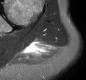
MRI of an extremity soft-tissue mass, one axial slice. Slice 19 of 30 in the series (ordered by position). STIR. MR volume resampled by the dataset authors to the PET/CT grid (not the native acquisition matrix). 3.27 mm slice thickness. 86 × 80 image matrix, field of view 84 × 78 mm. Female patient. Case-level facts recorded for this patient, not image findings: histological type: malignant fibrous histiocytoma; grade: low; site of the primary tumour: left arm.
Structures marked on this image (expert contour drawn on MRI and transferred to this co-registered scan by the dataset authors):
- gross tumour volume (mass): bounding box <26,42,41,54> (left, top, right, bottom; pixels)